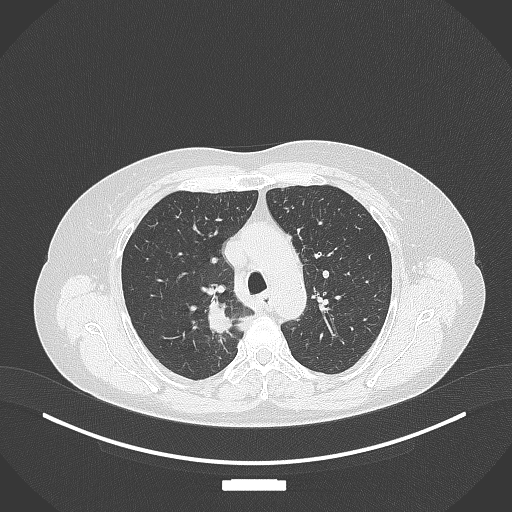
Chest CT, one axial slice. Reconstruction kernel B70f. Lung window (W 1500 / L -600 HU). 1 mm slice thickness. 512 × 512 image matrix, field of view 400 × 400 mm. Female patient, age 62 years. From the clinical record (not read from this slice): clinical TNM (as recorded): T1c N1 M0.
Structures marked on this image (bounding box drawn by a radiologist):
- lung tumour (recorded histology: squamous cell carcinoma): bounding box (x1, y1, x2, y2) in pixels: (202, 297, 232, 336)